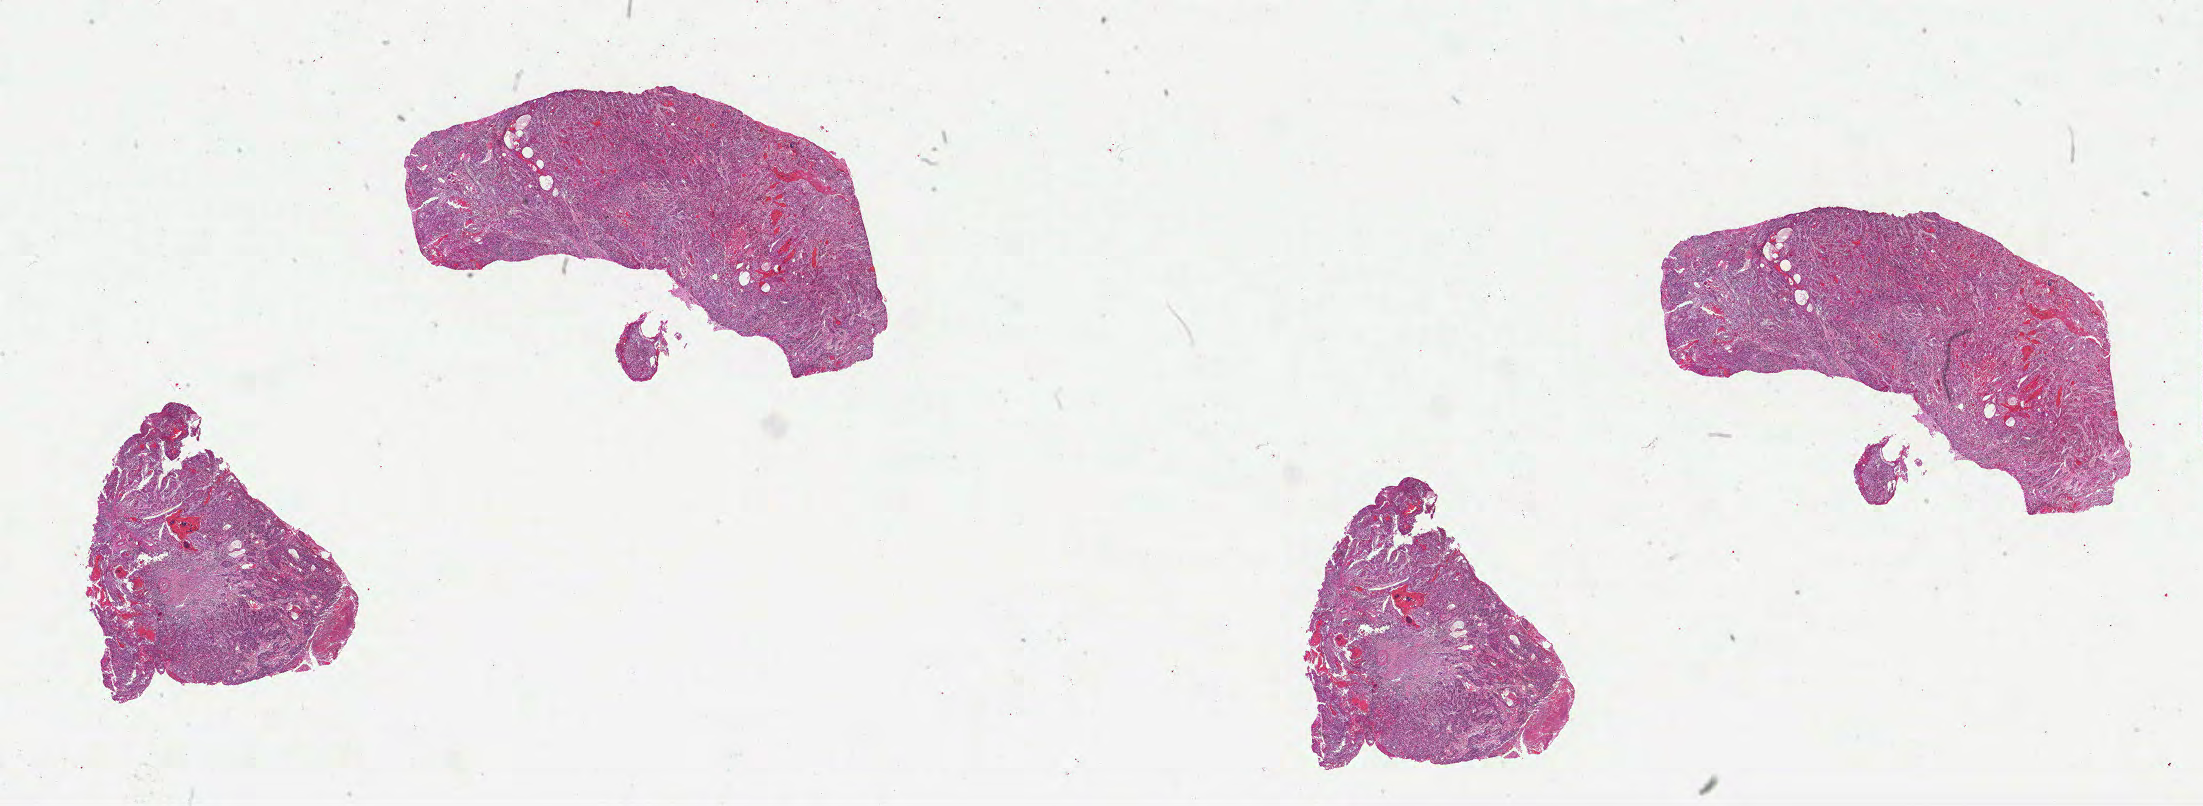
Whole-slide histology image, H&E — a low-resolution overview of the entire scanned area, about 35.7 x 13.1 mm, FFPE section, sample: primary tumour, head and neck. Patient: male, age at initial diagnosis 47 years. Histologic grade: G2 (moderately differentiated).
* pathologic diagnosis: Squamous cell carcinoma, NOS (floor of mouth, NOS)
* AJCC pathologic stage: IVA